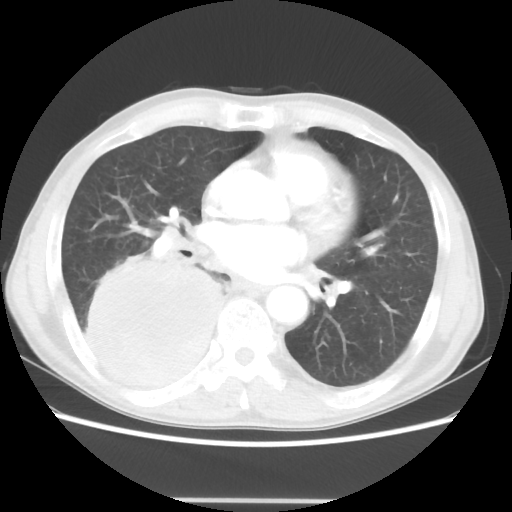
Chest CT, one axial slice; position 21 of 48 along the scan axis; reconstruction kernel STANDARD; lung window (W 1500 / L -600 HU); 512 × 512 image matrix, field of view 361 × 361 mm. Patient: male, 66 years. From the clinical record (not read from this slice): clinical TNM (as recorded): T4 N1 M1; histopathological grade: G3.
Outlined on this slice (bounding box drawn by a radiologist):
- lung tumour (recorded histology: small cell carcinoma): bounding box <77,248,222,395> (left, top, right, bottom; pixels)